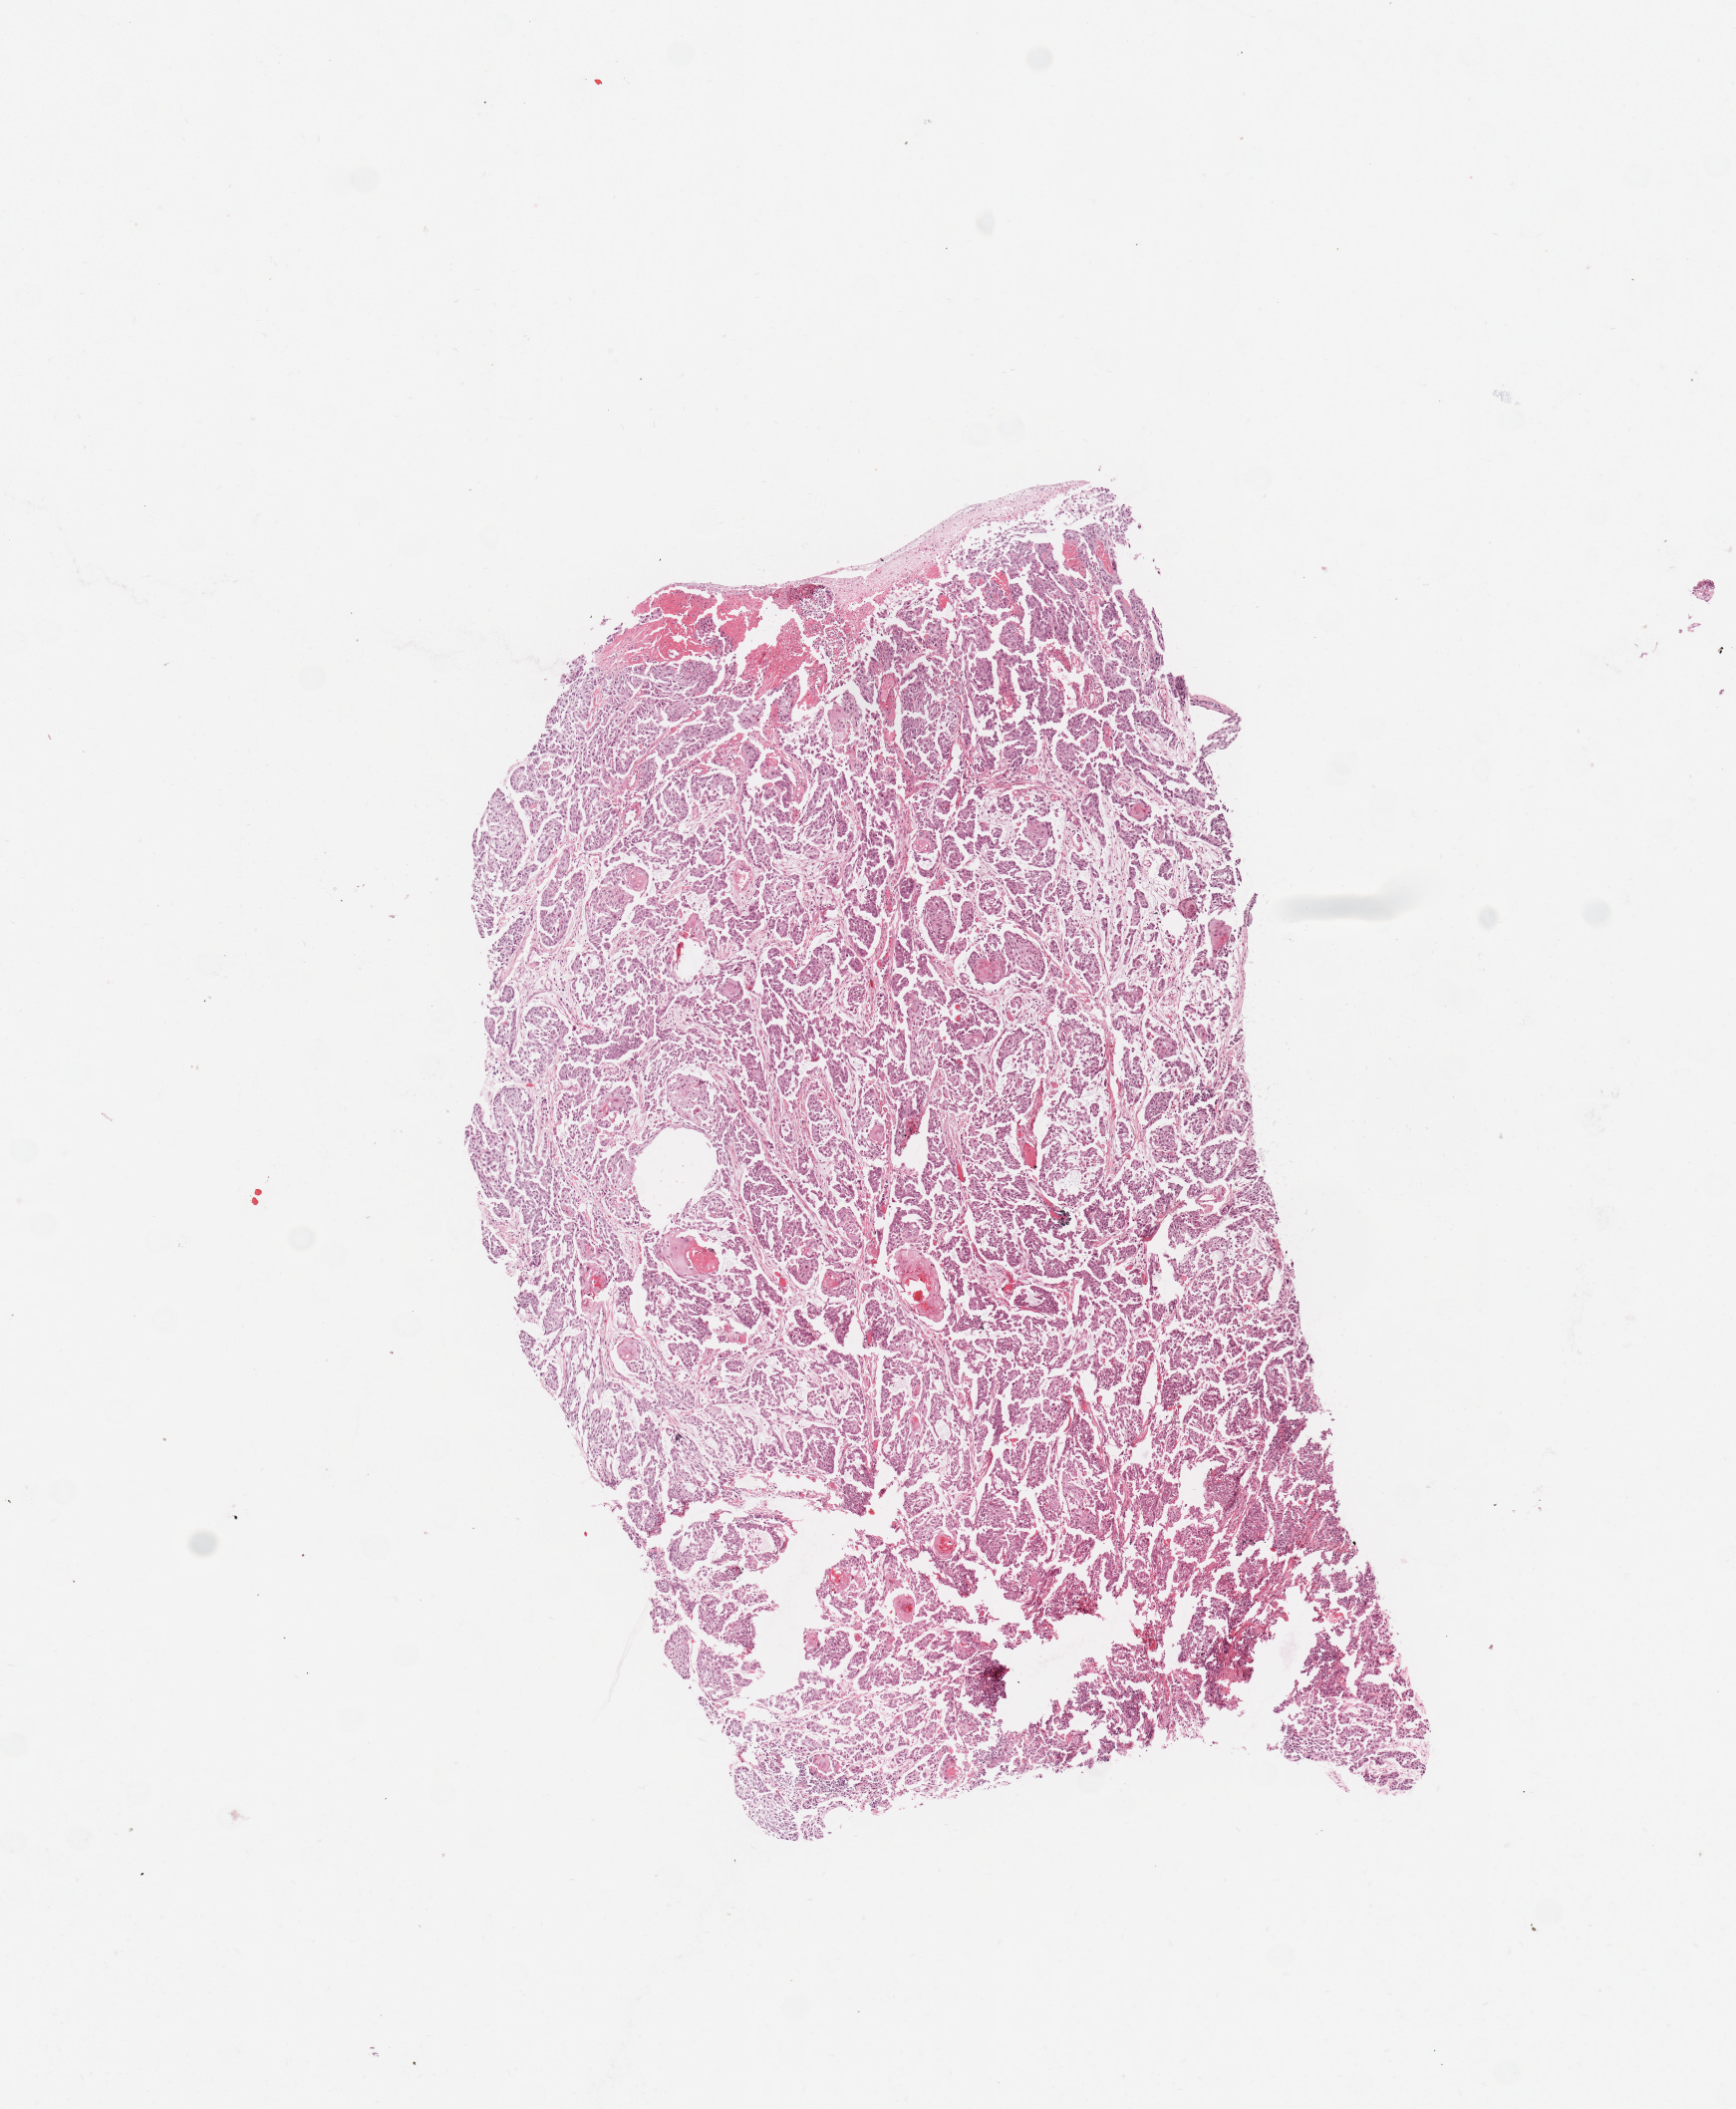
Whole-slide histology image, H&E-stained — low-resolution overview of the scanned area, about 6.9 x 8.4 mm (slide scanned at 20x), tumour tissue sample, sampled site: supraglottis. Male, 59 y/o. Histologic grade: G3 (poorly differentiated). Slide review estimates, as recorded: tumour nuclei 90%, necrosis 3%.
- AJCC pathologic stage: III
- histologic diagnosis: Squamous cell carcinoma, NOS